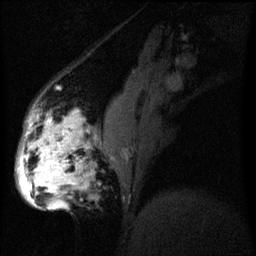
Breast MRI (dynamic contrast-enhanced), one sagittal slice. Slice 20 of 60 in the series (ordered by position). Dynamic contrast-enhanced series, image 2 of 3 at this slice position (ordered by acquisition). 1.5 T. TE 4.2 ms, TR 8 ms. 2.2 mm slice thickness. 256 × 256 image matrix, field of view 200 × 200 mm. Female patient, age 50 years.
Annotated regions visible in this slice (semi-automatically segmented with operator editing):
- analysis volume of interest (the breast-tissue region the enhancement analysis was run in; not a lesion): bounding box [x1, y1, x2, y2] px = [19, 112, 93, 211]
- tumour enhancement mask (voxels above the 70 % enhancement threshold inside the analysis volume of interest): [19, 118, 77, 209]